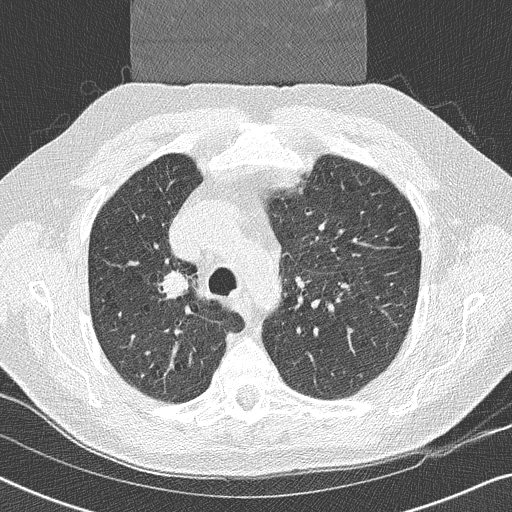
Axial slice from a low-dose chest CT screening exam; second screening round (one year after baseline); lung window (W 1500 / L -600 HU); 2 mm slice thickness; 120 kVp. Male participant, aged 59 years at enrolment. Former smoker at enrolment.
Expert reader's lesion annotation, bounding box [x1, y1, x2, y2] px = [144, 256, 204, 308]. The exam's reader record, not a measurement of the box and not confirmed to be the same lesion: non-calcified nodule or mass ≥4 mm, right upper lobe, 17 × 16 mm, smooth margins, soft tissue attenuation, pre-existing on the prior screen: yes.